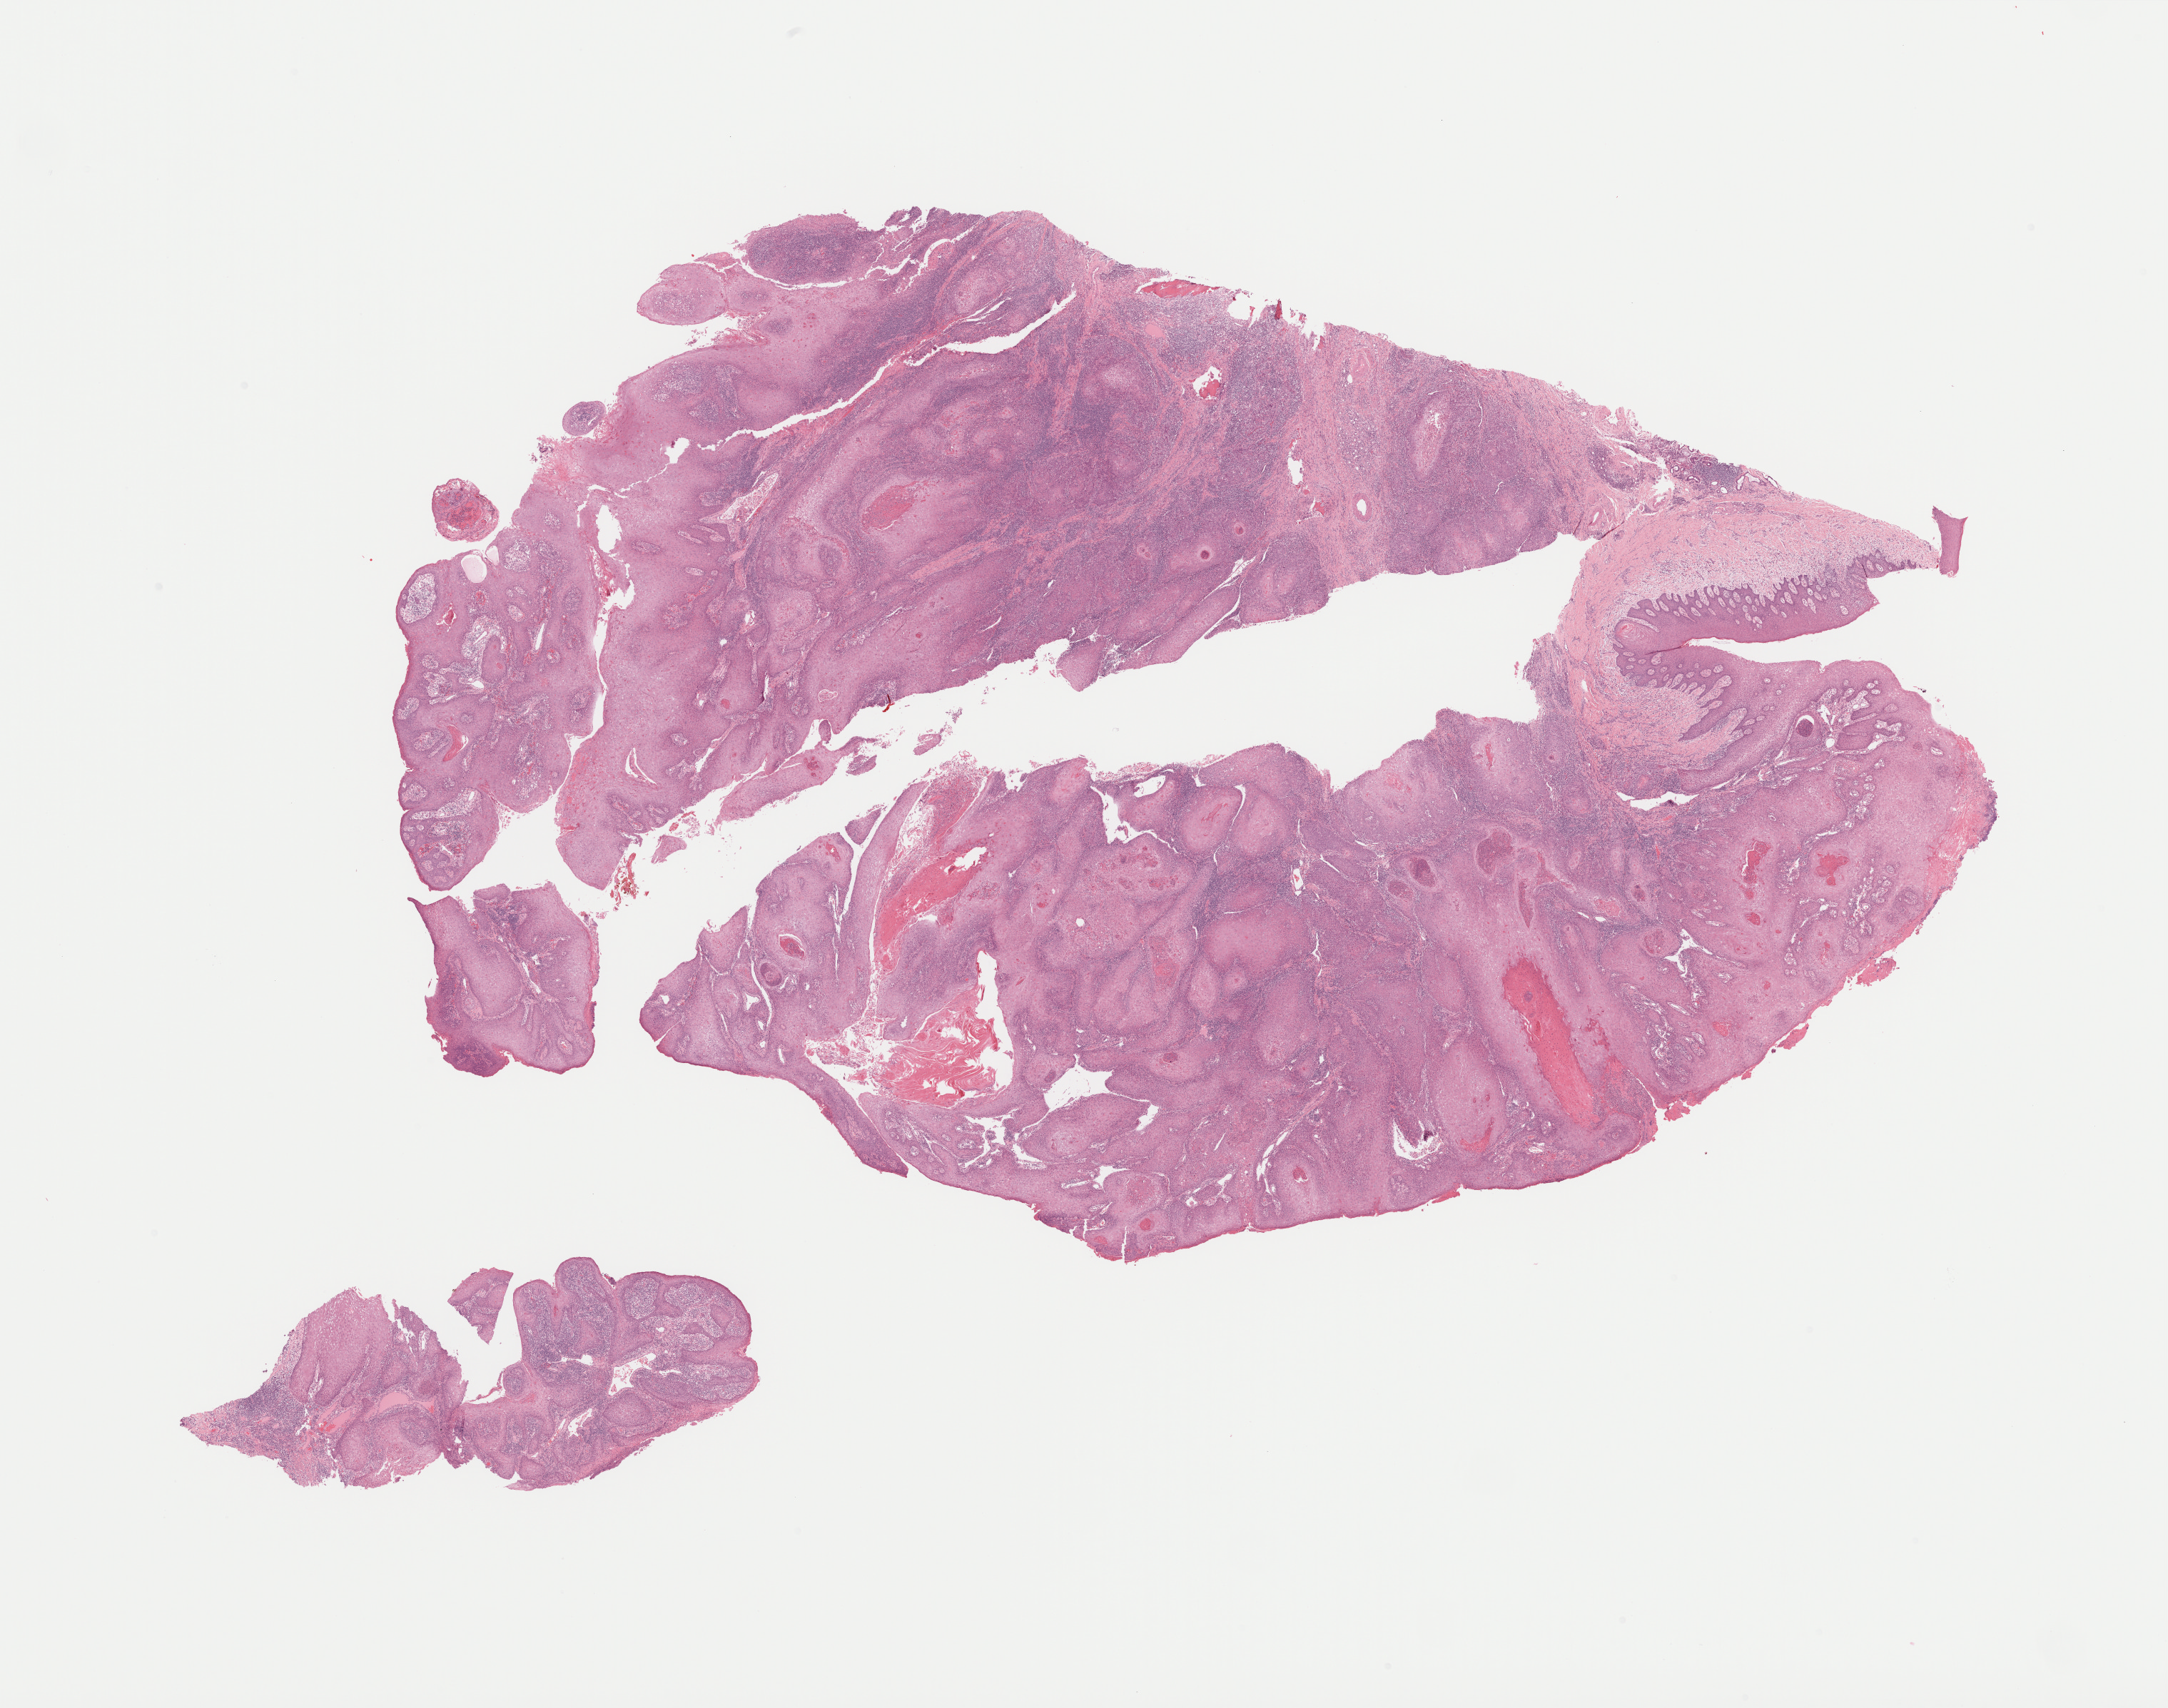
H&E whole-slide image — shown as a low-resolution overview of the whole scanned area (about 24.5 x 19.3 mm, from a 40x scan); FFPE section; head and neck, primary tumour sample. Patient: female, age at initial diagnosis 73 years. Histologic grade: G2 (moderately differentiated).
Laterality: right. Histologic diagnosis: Squamous cell carcinoma, NOS (overlapping lesion of lip, oral cavity and pharynx).